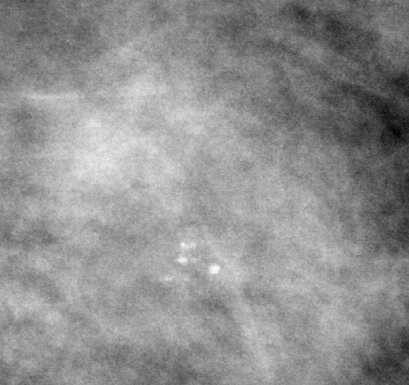
Crop from a digitized film mammogram around one marked abnormality; left breast; MLO view.
- Marked abnormality: calcifications, morphology punctate, distribution clustered; BI-RADS assessment category 3; subtlety rating 3 on a 1 (subtle) to 5 (obvious) scale; pathology (as recorded): benign.